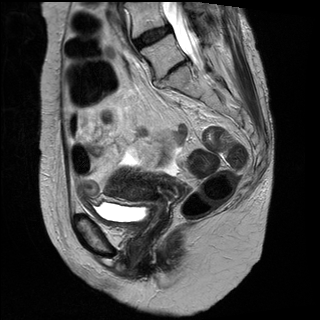
Pelvic MRI for cervical cancer, one sagittal slice; position 14 of 31 along the scan axis; T2-weighted; 1.5 T; TE 89 ms, TR 3890 ms; 4 mm slice thickness; 320 × 320 image matrix. Patient: female, 61 years.
Outlined on this slice (expert manual segmentation):
- uterus and cervix: box from (x=103, y=171) to (x=188, y=207) px